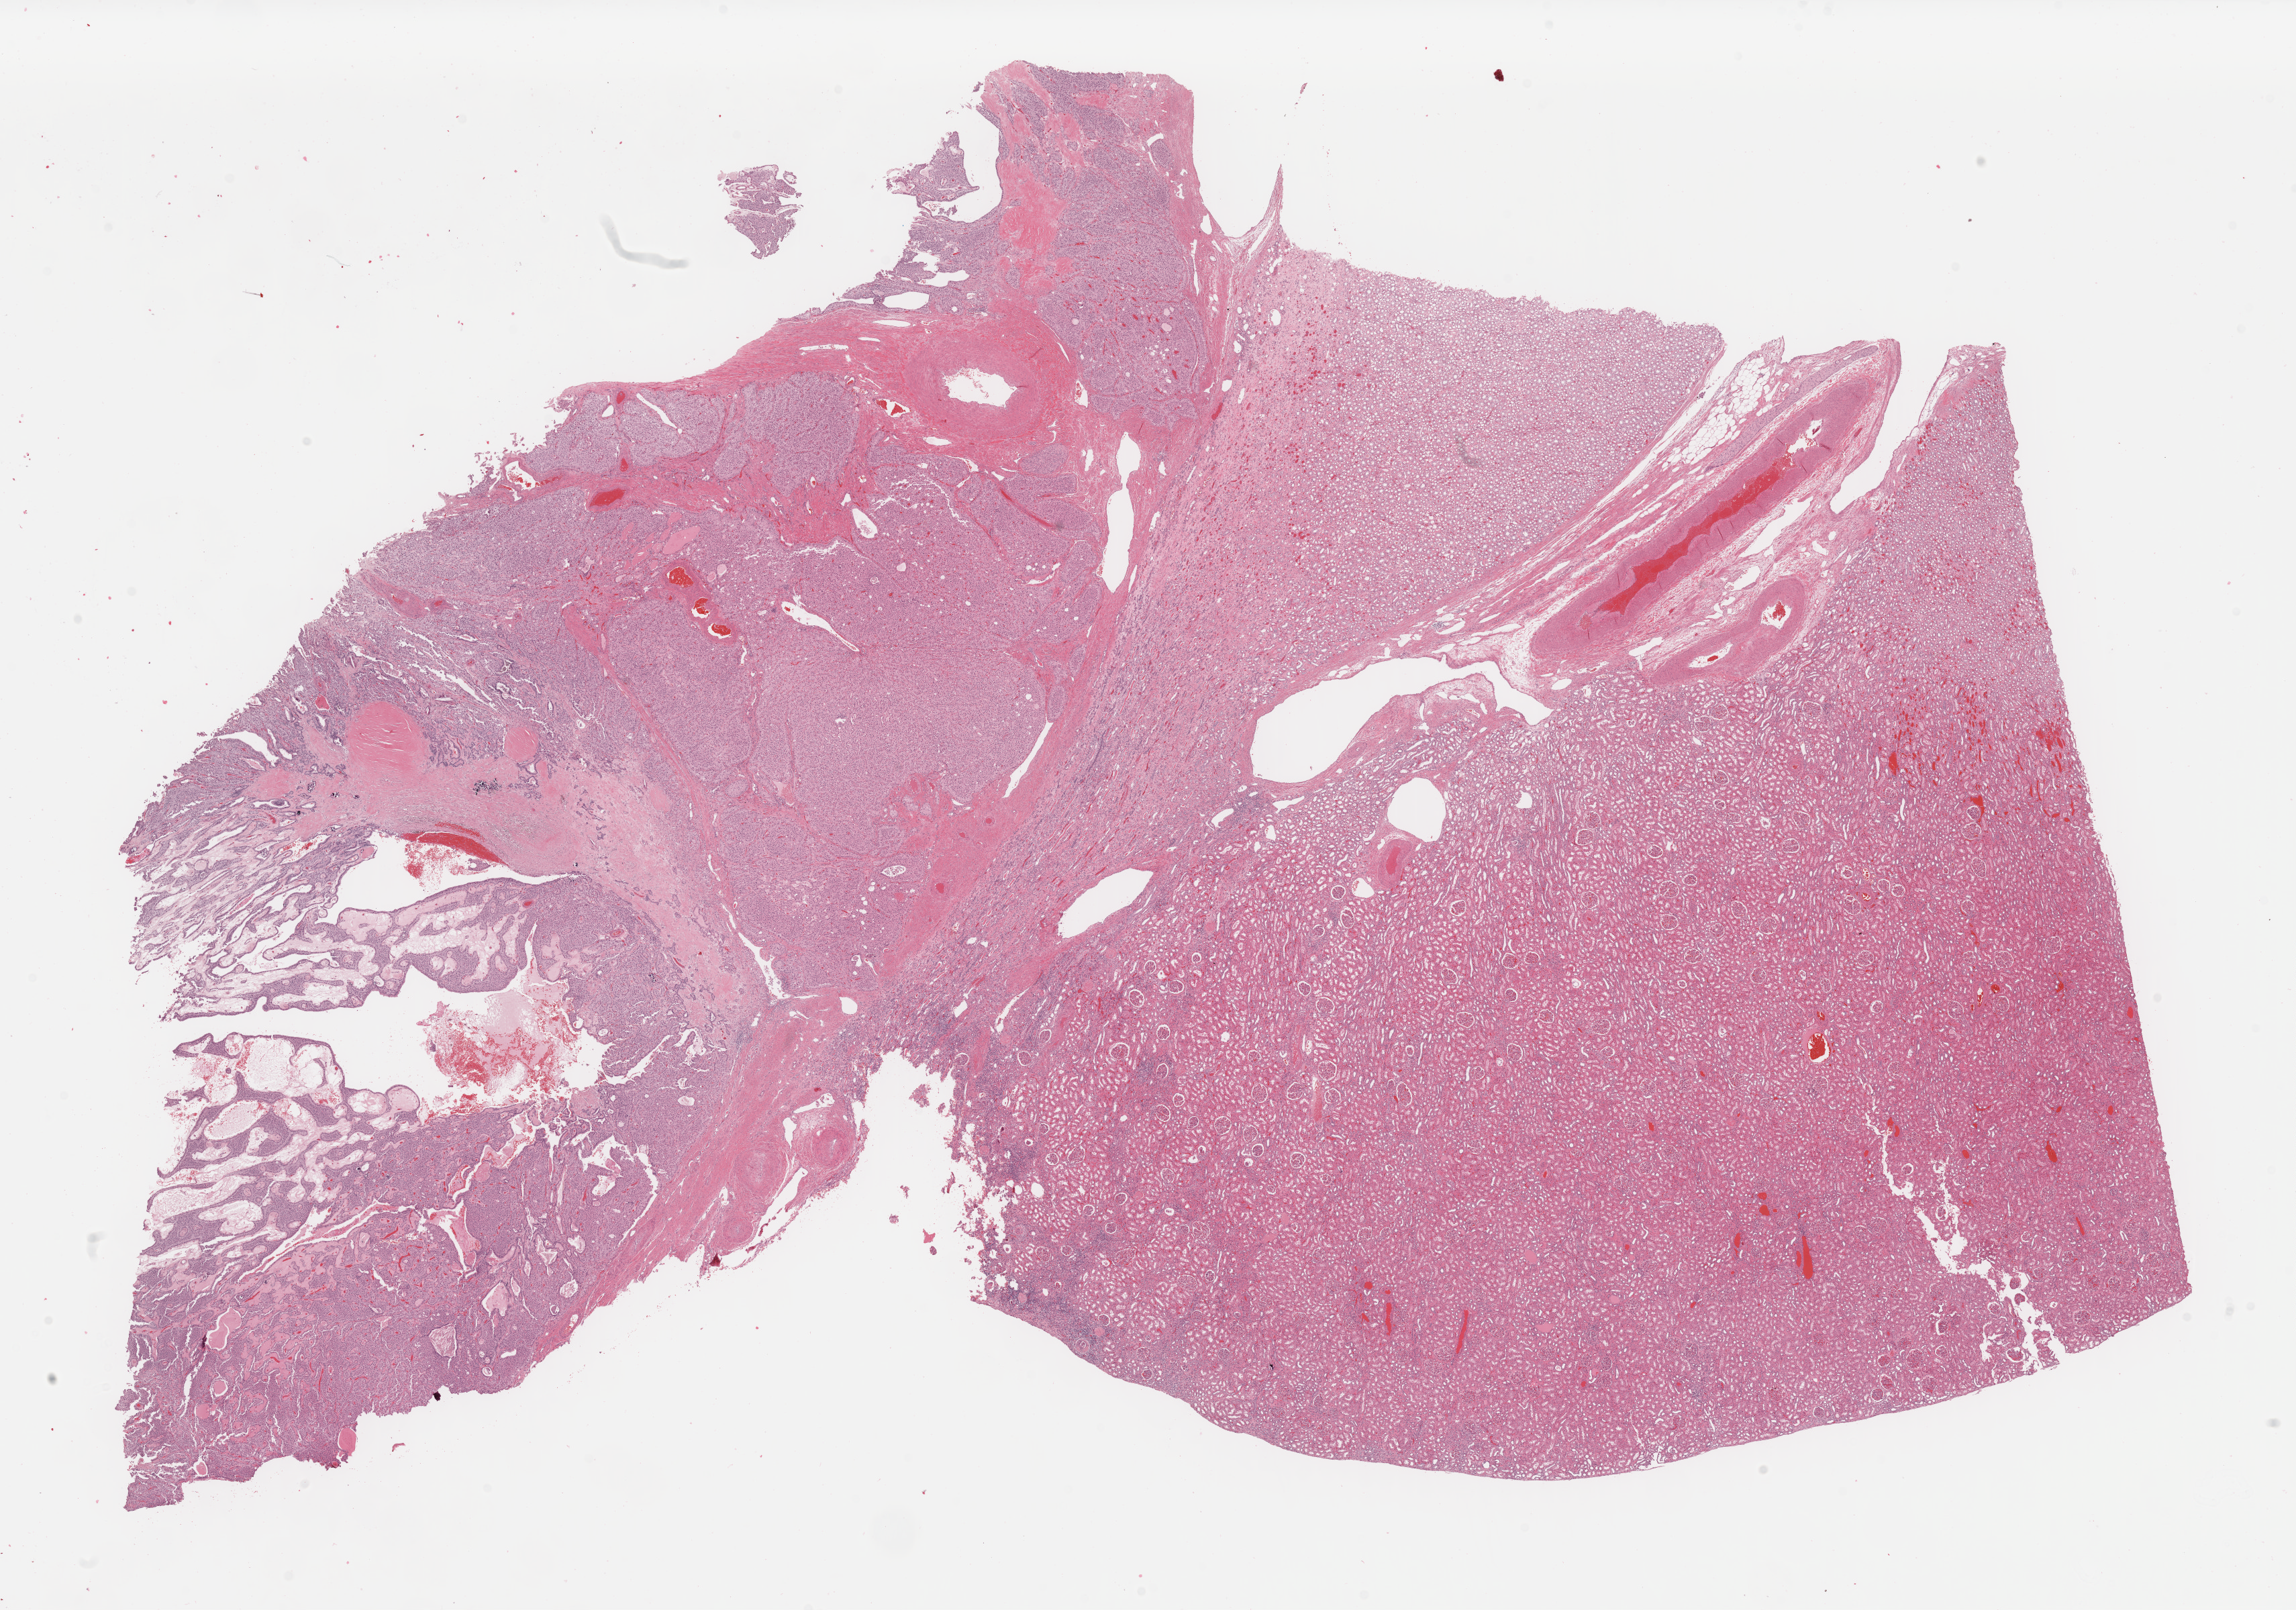
Digitized H&E tissue section (whole slide), a low-resolution overview of the entire scanned area, about 27.1 x 19.0 mm (acquisition: 40x scan), FFPE section, primary tumour sample from the kidney. Female, age 44 years at initial diagnosis. Slide review estimates, as recorded: tumour cells 55%, tumour nuclei 55%, normal cells 30%, stromal cells 15%, necrosis 0%. Infiltration values recorded for this section: lymphocyte infiltration 0%, monocyte infiltration 0%, neutrophil infiltration 0%.
Histologic diagnosis: Renal cell carcinoma, chromophobe type. AJCC pathologic stage: IV. Lymph nodes positive (case pathology): 0 of 1 examined.